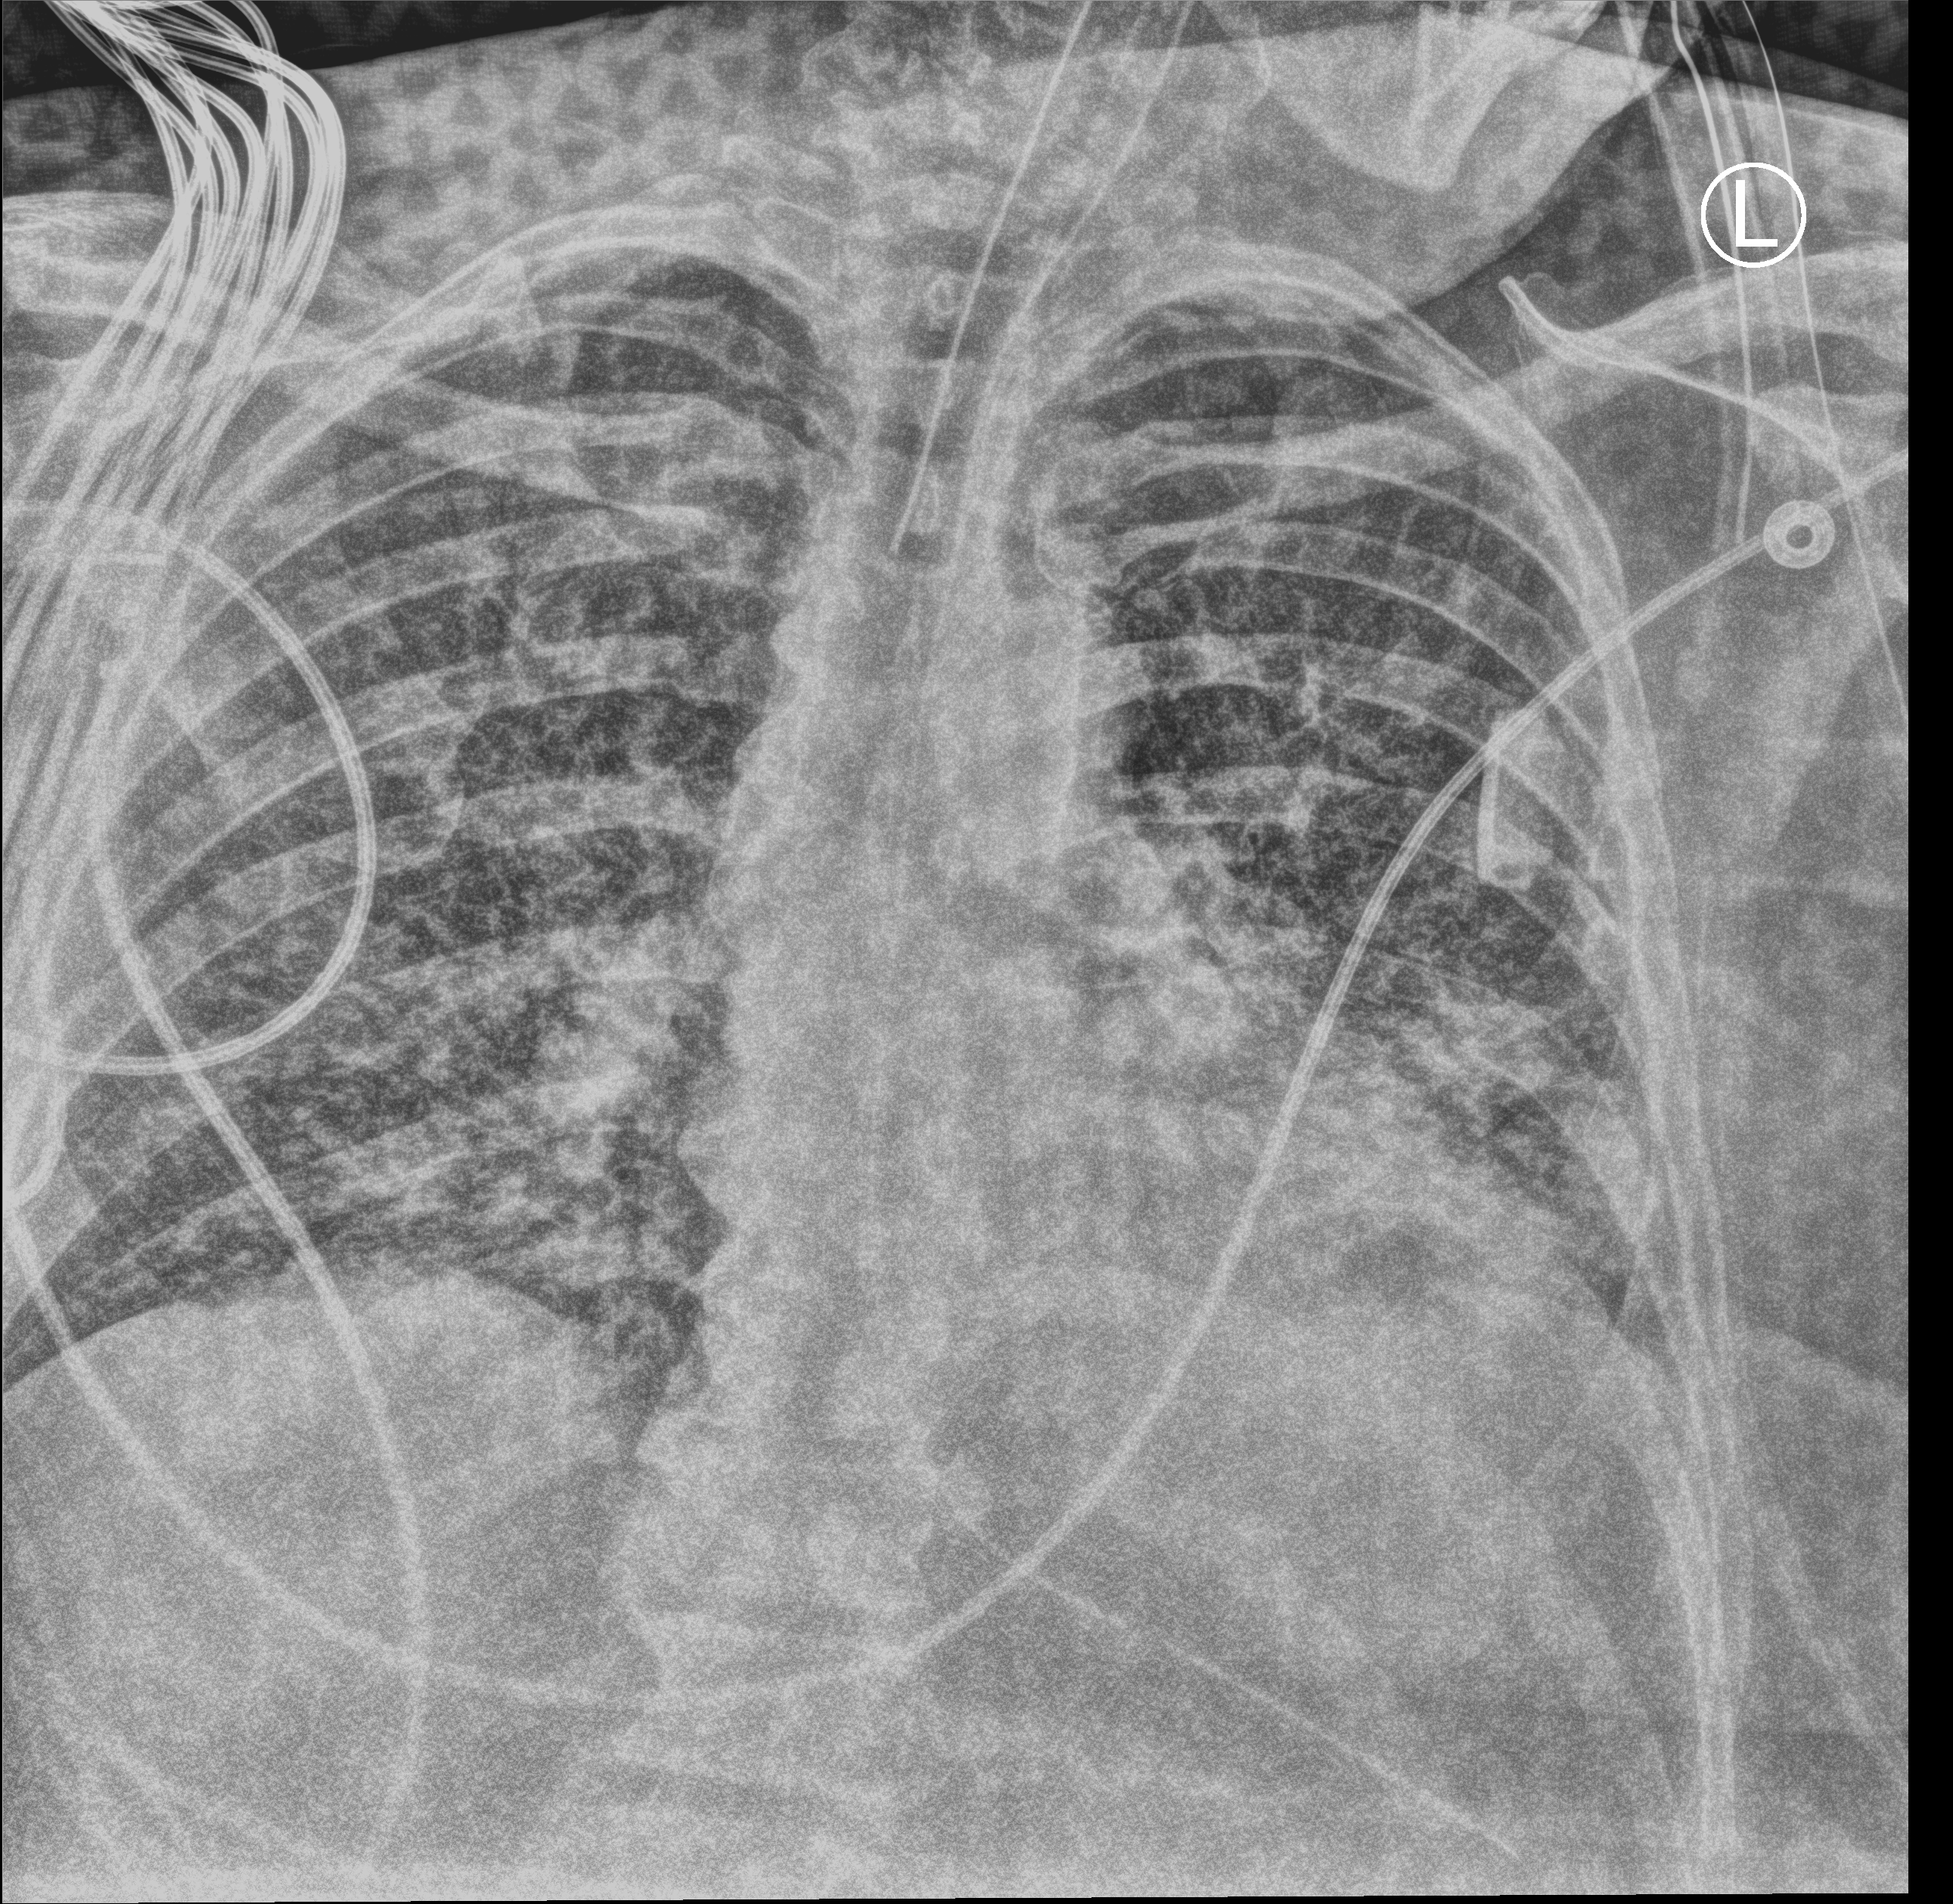
Bedside chest radiograph (computed radiography); anteroposterior (AP) projection. Adult patient hospitalised with COVID-19, age 18–59 years.
Admission-level facts for this patient (not findings on this image; timing relative to this image not recorded): admitted to intensive care during this hospital stay: yes.